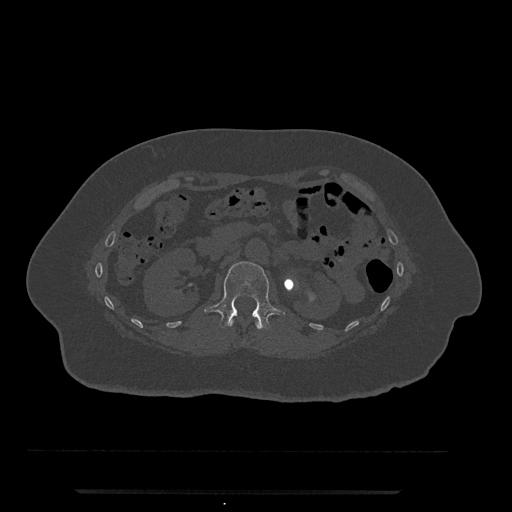
CT including the spine, one axial slice. Slice 115 of 797 in the series (ordered by position). Reconstruction kernel Br40s/3. 120 kVp. Bone window (W 1800 / L 400 HU). 0.5 mm slice thickness. 512 × 512 image matrix. Patient: female, 51 years. From the clinical record (not read from this slice): primary cancer: neuro.
Annotated regions visible in this slice (semi-automatic segmentation, software-assisted and operator-edited):
- L1 vertebra: bounding box (x1, y1, x2, y2) in pixels: (204, 261, 285, 330)
- T12 vertebra: (230, 319, 261, 330)